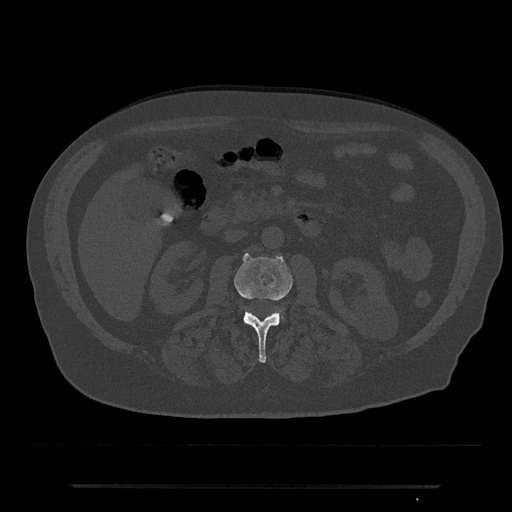
CT including the spine, one axial slice. Slice 459 of 797 in the series (ordered by position). Reconstruction kernel Br40s/3. 120 kVp. Bone window (W 1800 / L 400 HU). 512 × 512 image matrix, field of view 434 × 434 mm. Patient: male, 80 years. Case-level facts recorded for this patient, not image findings: primary cancer: prostate; vertebrae with lytic lesions (as recorded): L1, T11.
Structures marked on this image (semi-automatically segmented with operator editing):
- L2 vertebra: bounding box (x1, y1, x2, y2) in pixels: (234, 253, 293, 363)